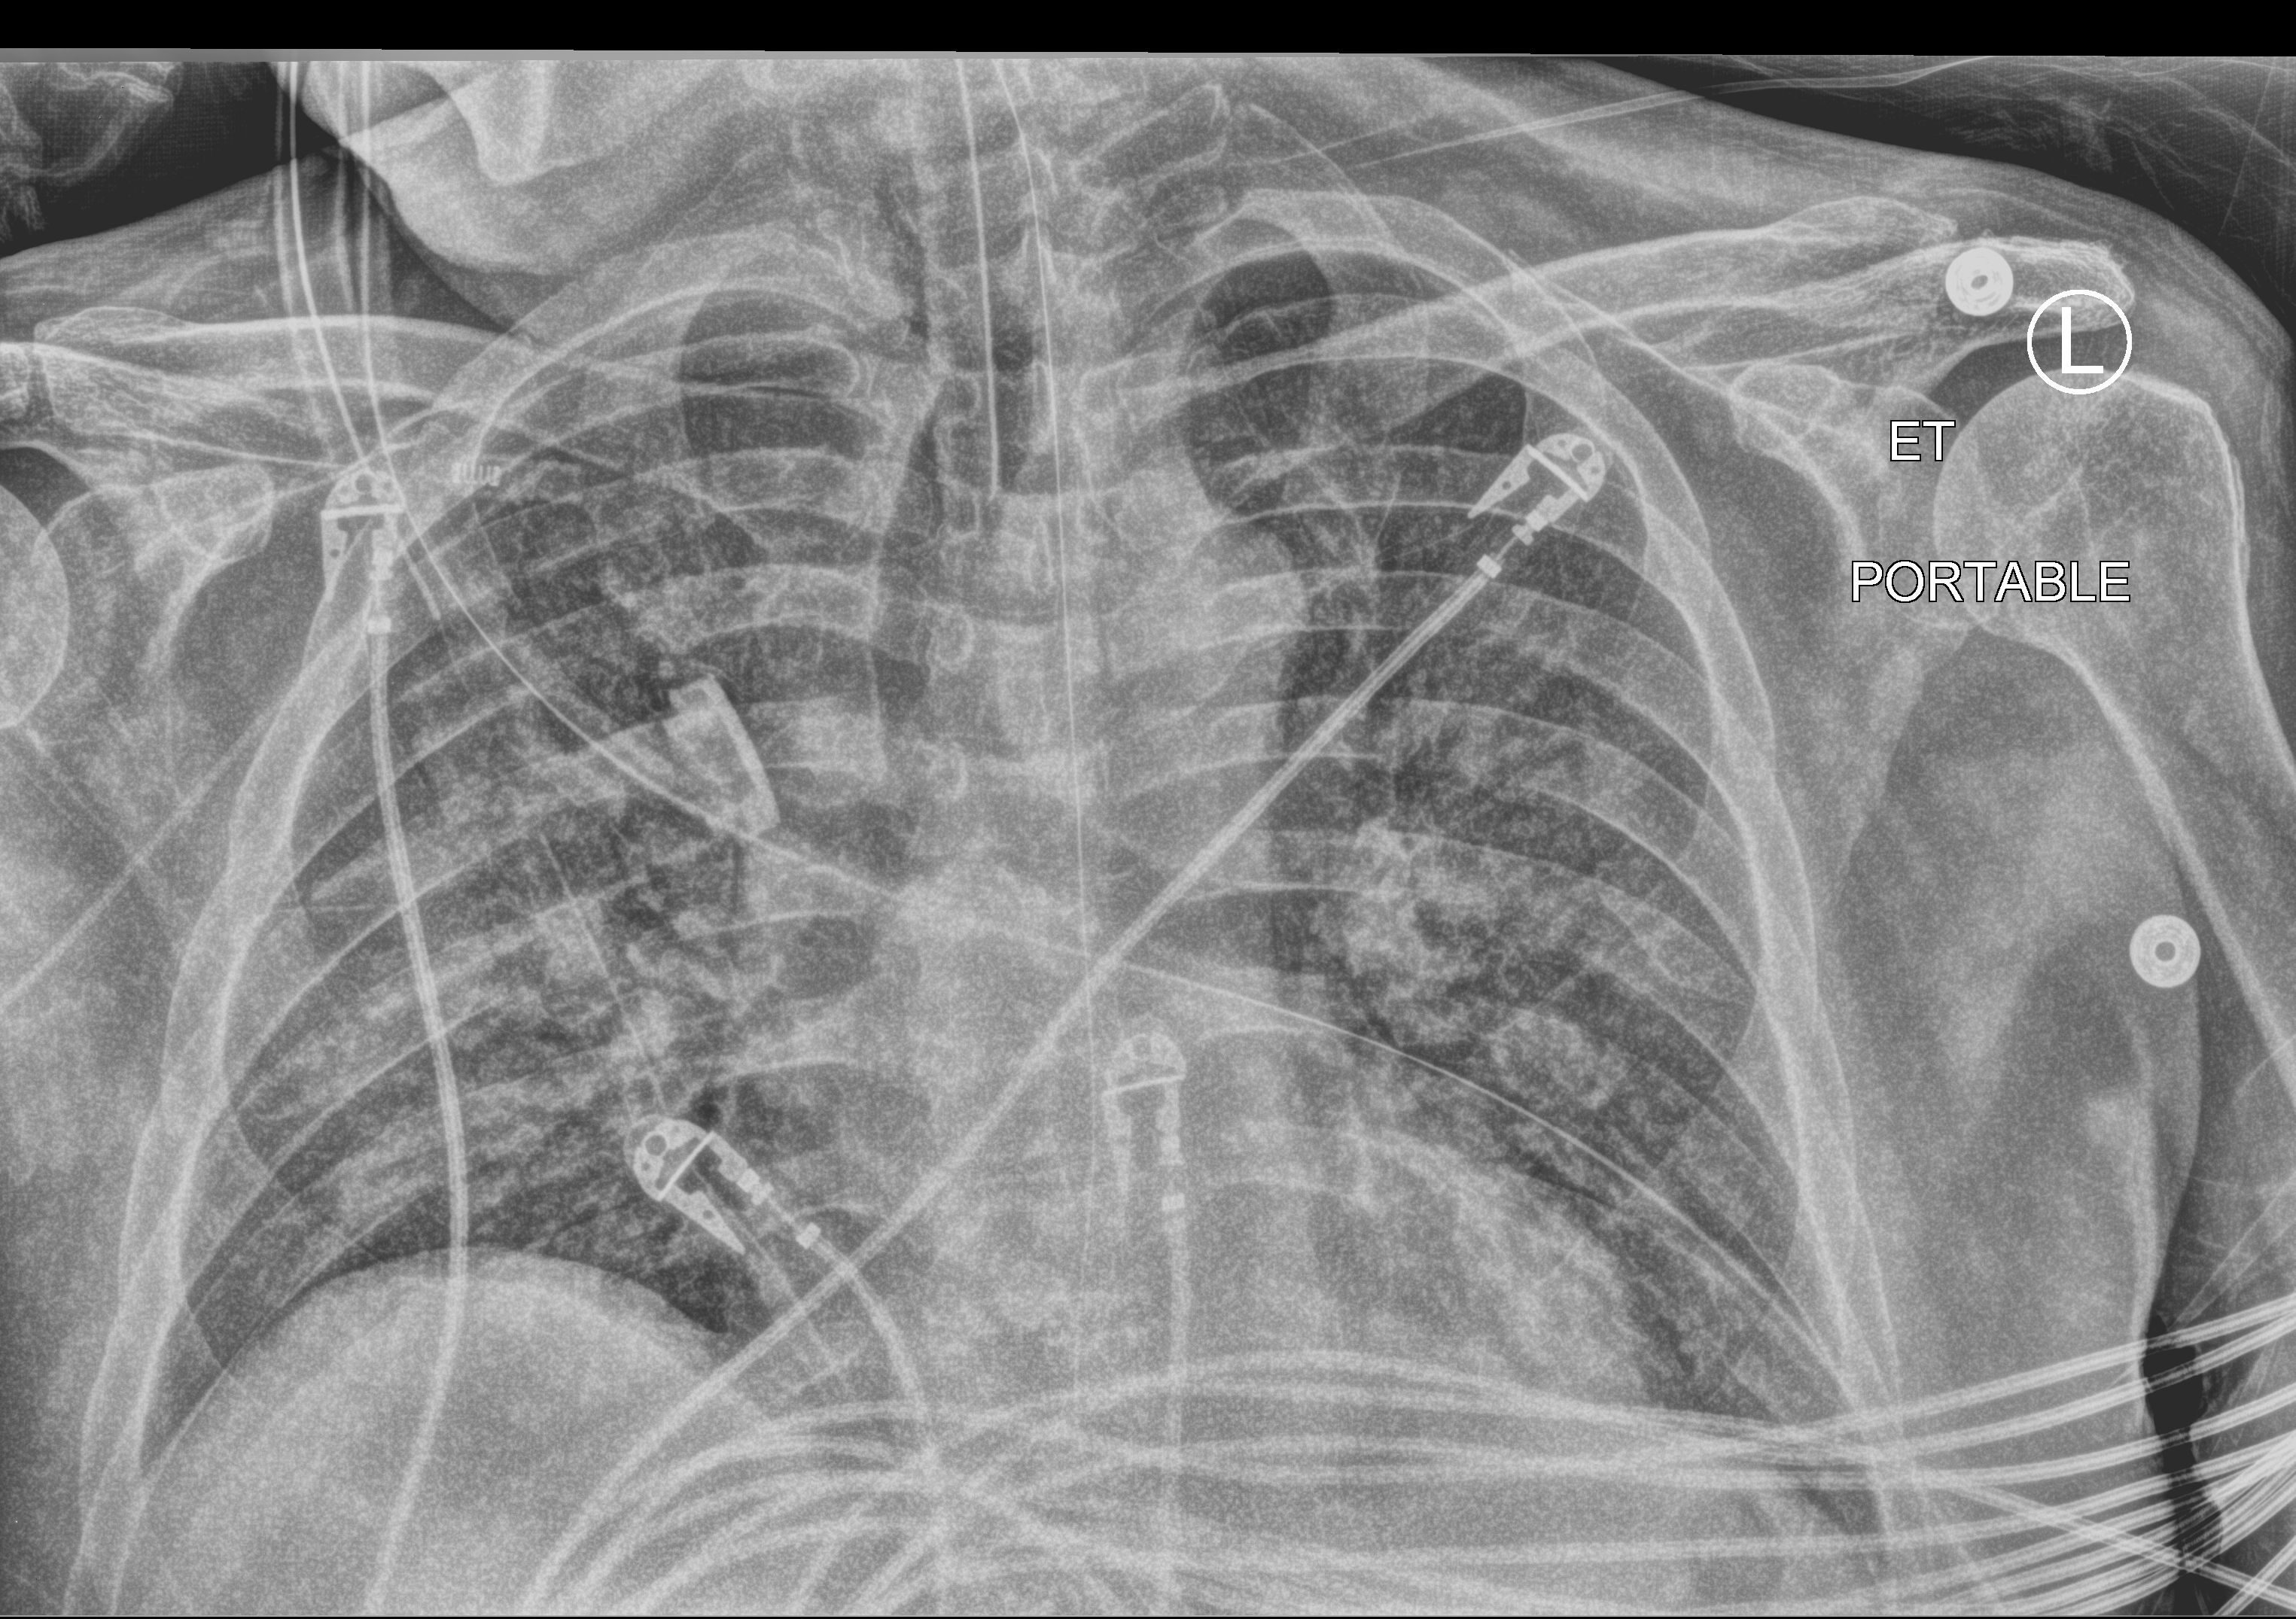
Chest X-ray (portable); anteroposterior (AP) projection. Male patient hospitalised with COVID-19, age 60–74 years.
Admission-level facts for this patient (not findings on this image; timing relative to this image not recorded): other chronic lung disease (admission record): no; admitted to intensive care during this hospital stay: yes.